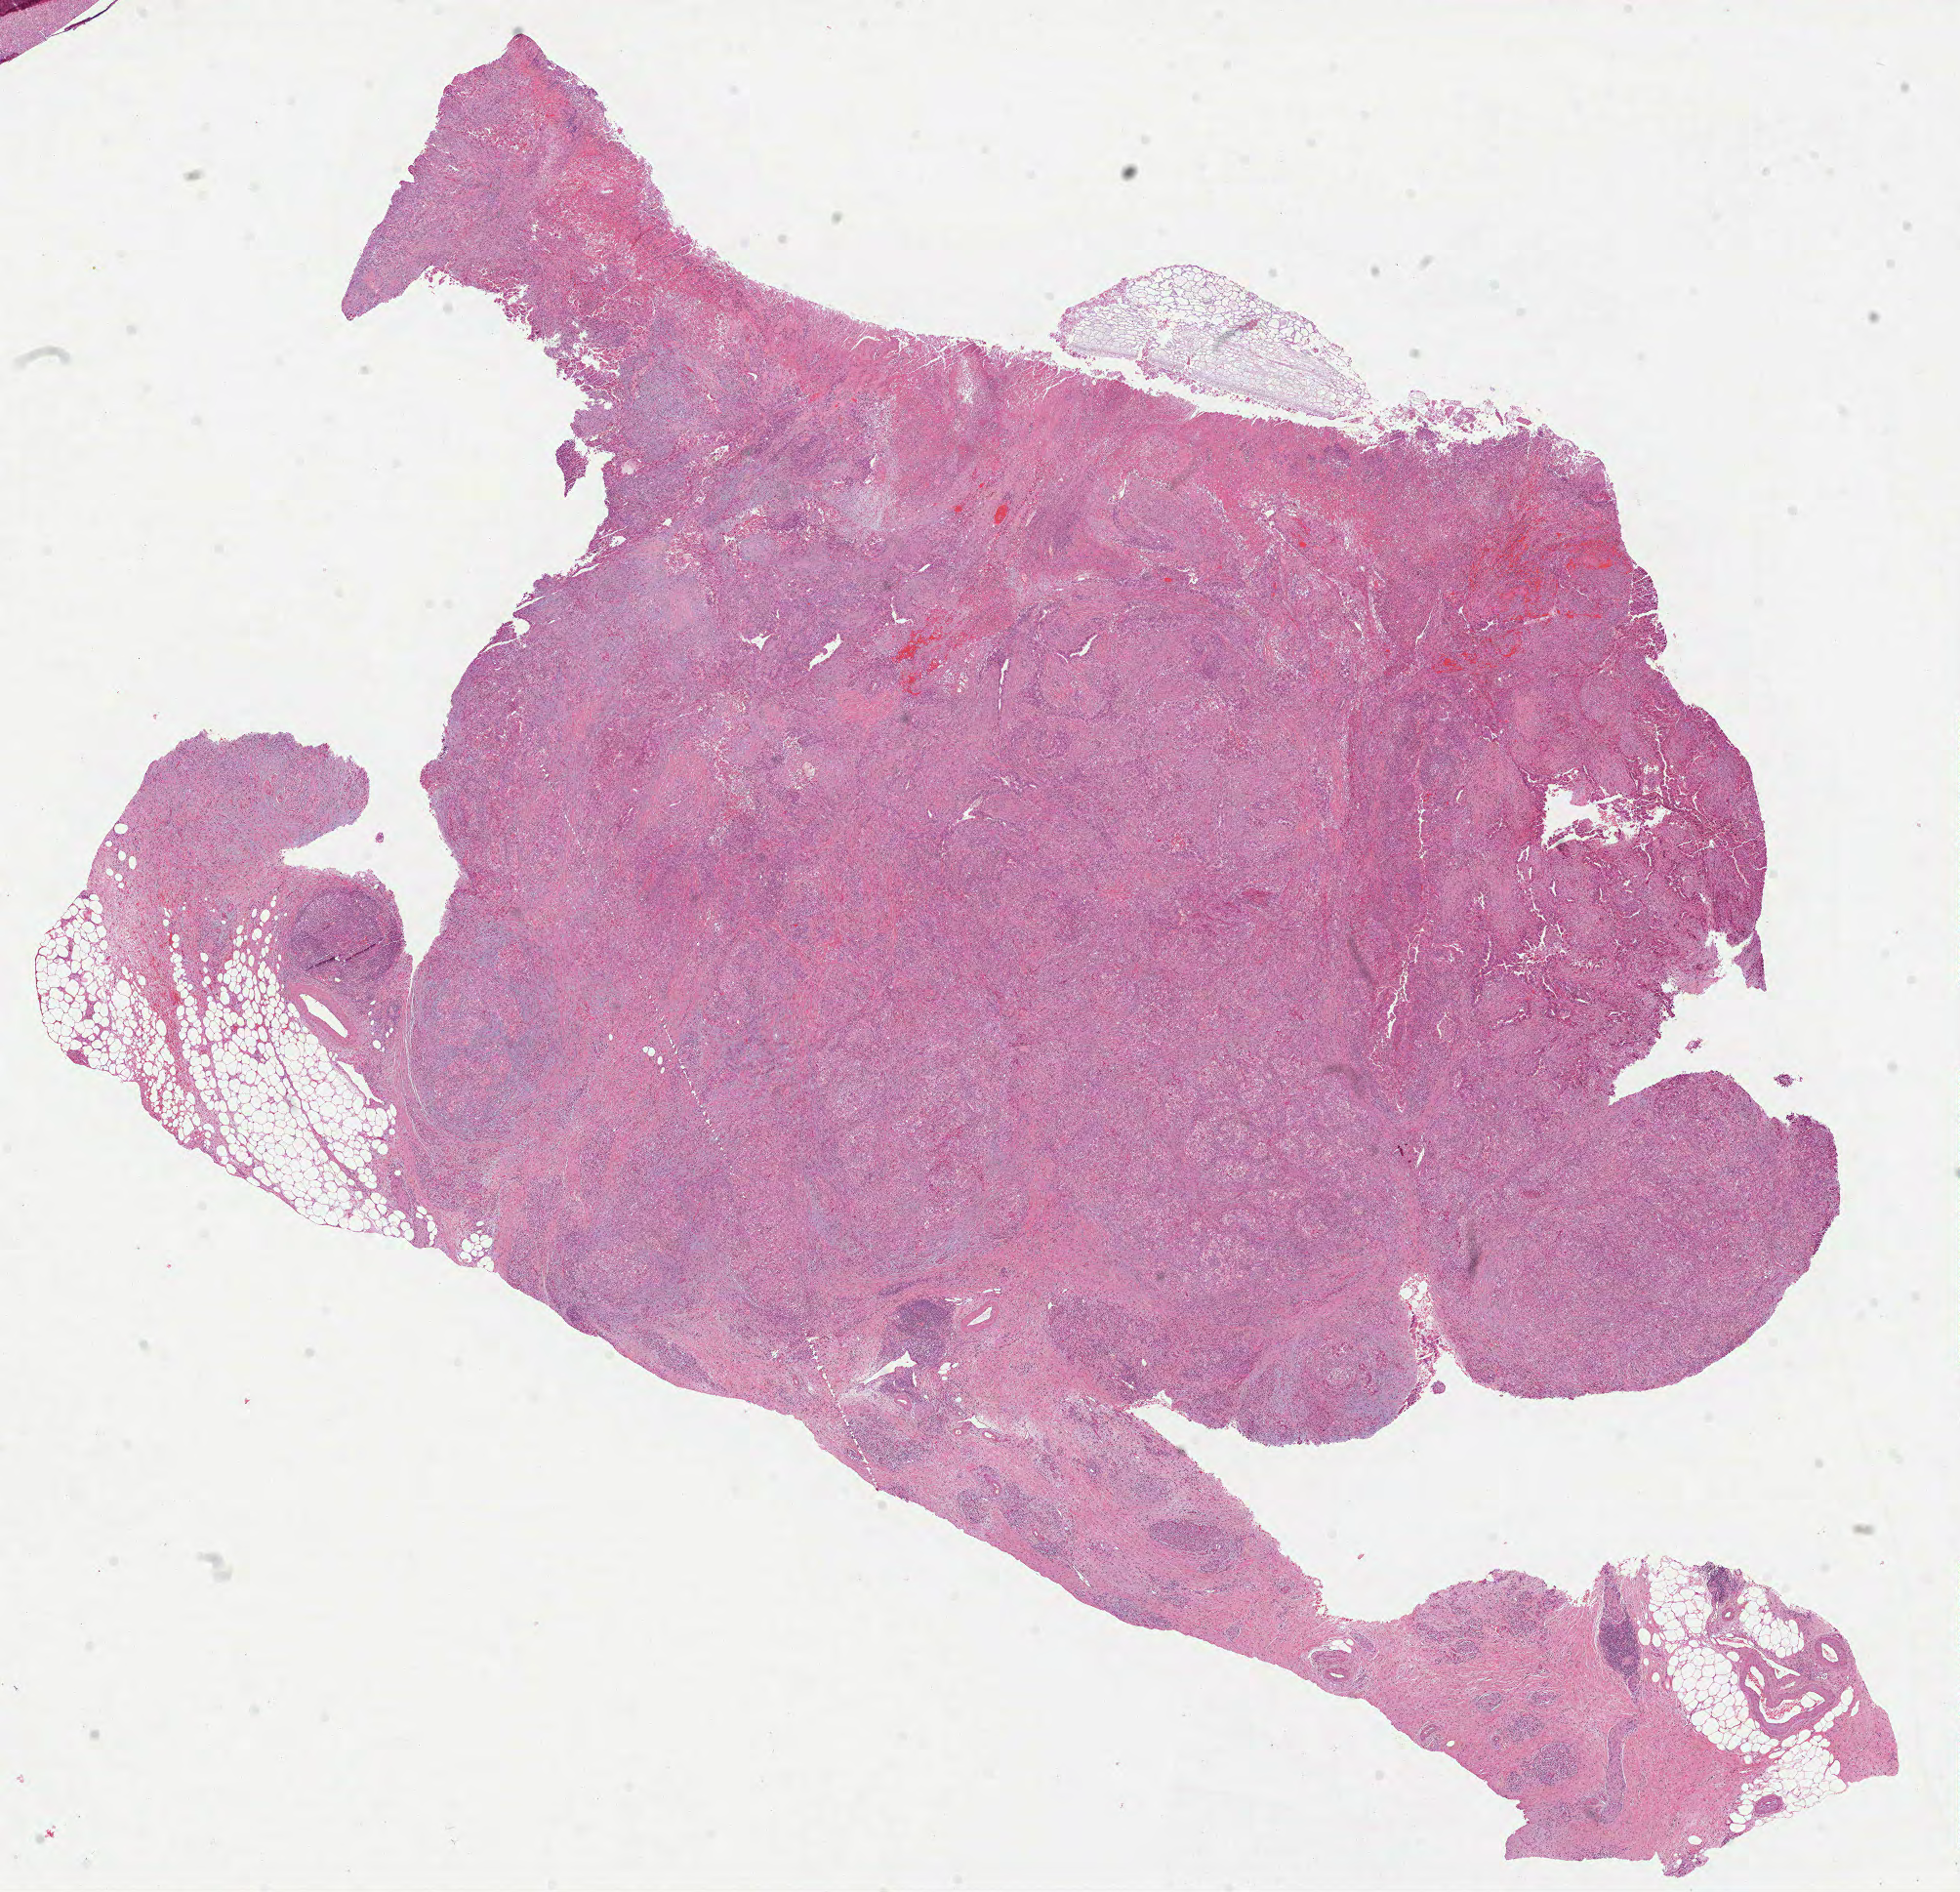
H&E whole-slide image — shown as a low-resolution overview of the whole scanned area (about 16.2 x 15.6 mm, acquisition: 40x scan); formalin-fixed paraffin-embedded (FFPE) diagnostic section; primary tumour sample from the pancreas. Female patient; age at initial diagnosis 76 years. Histologic grade: G3 (poorly differentiated).
• AJCC pathologic stage: IIB (7th edition)
• diagnosis: Infiltrating duct carcinoma, NOS (head of pancreas)